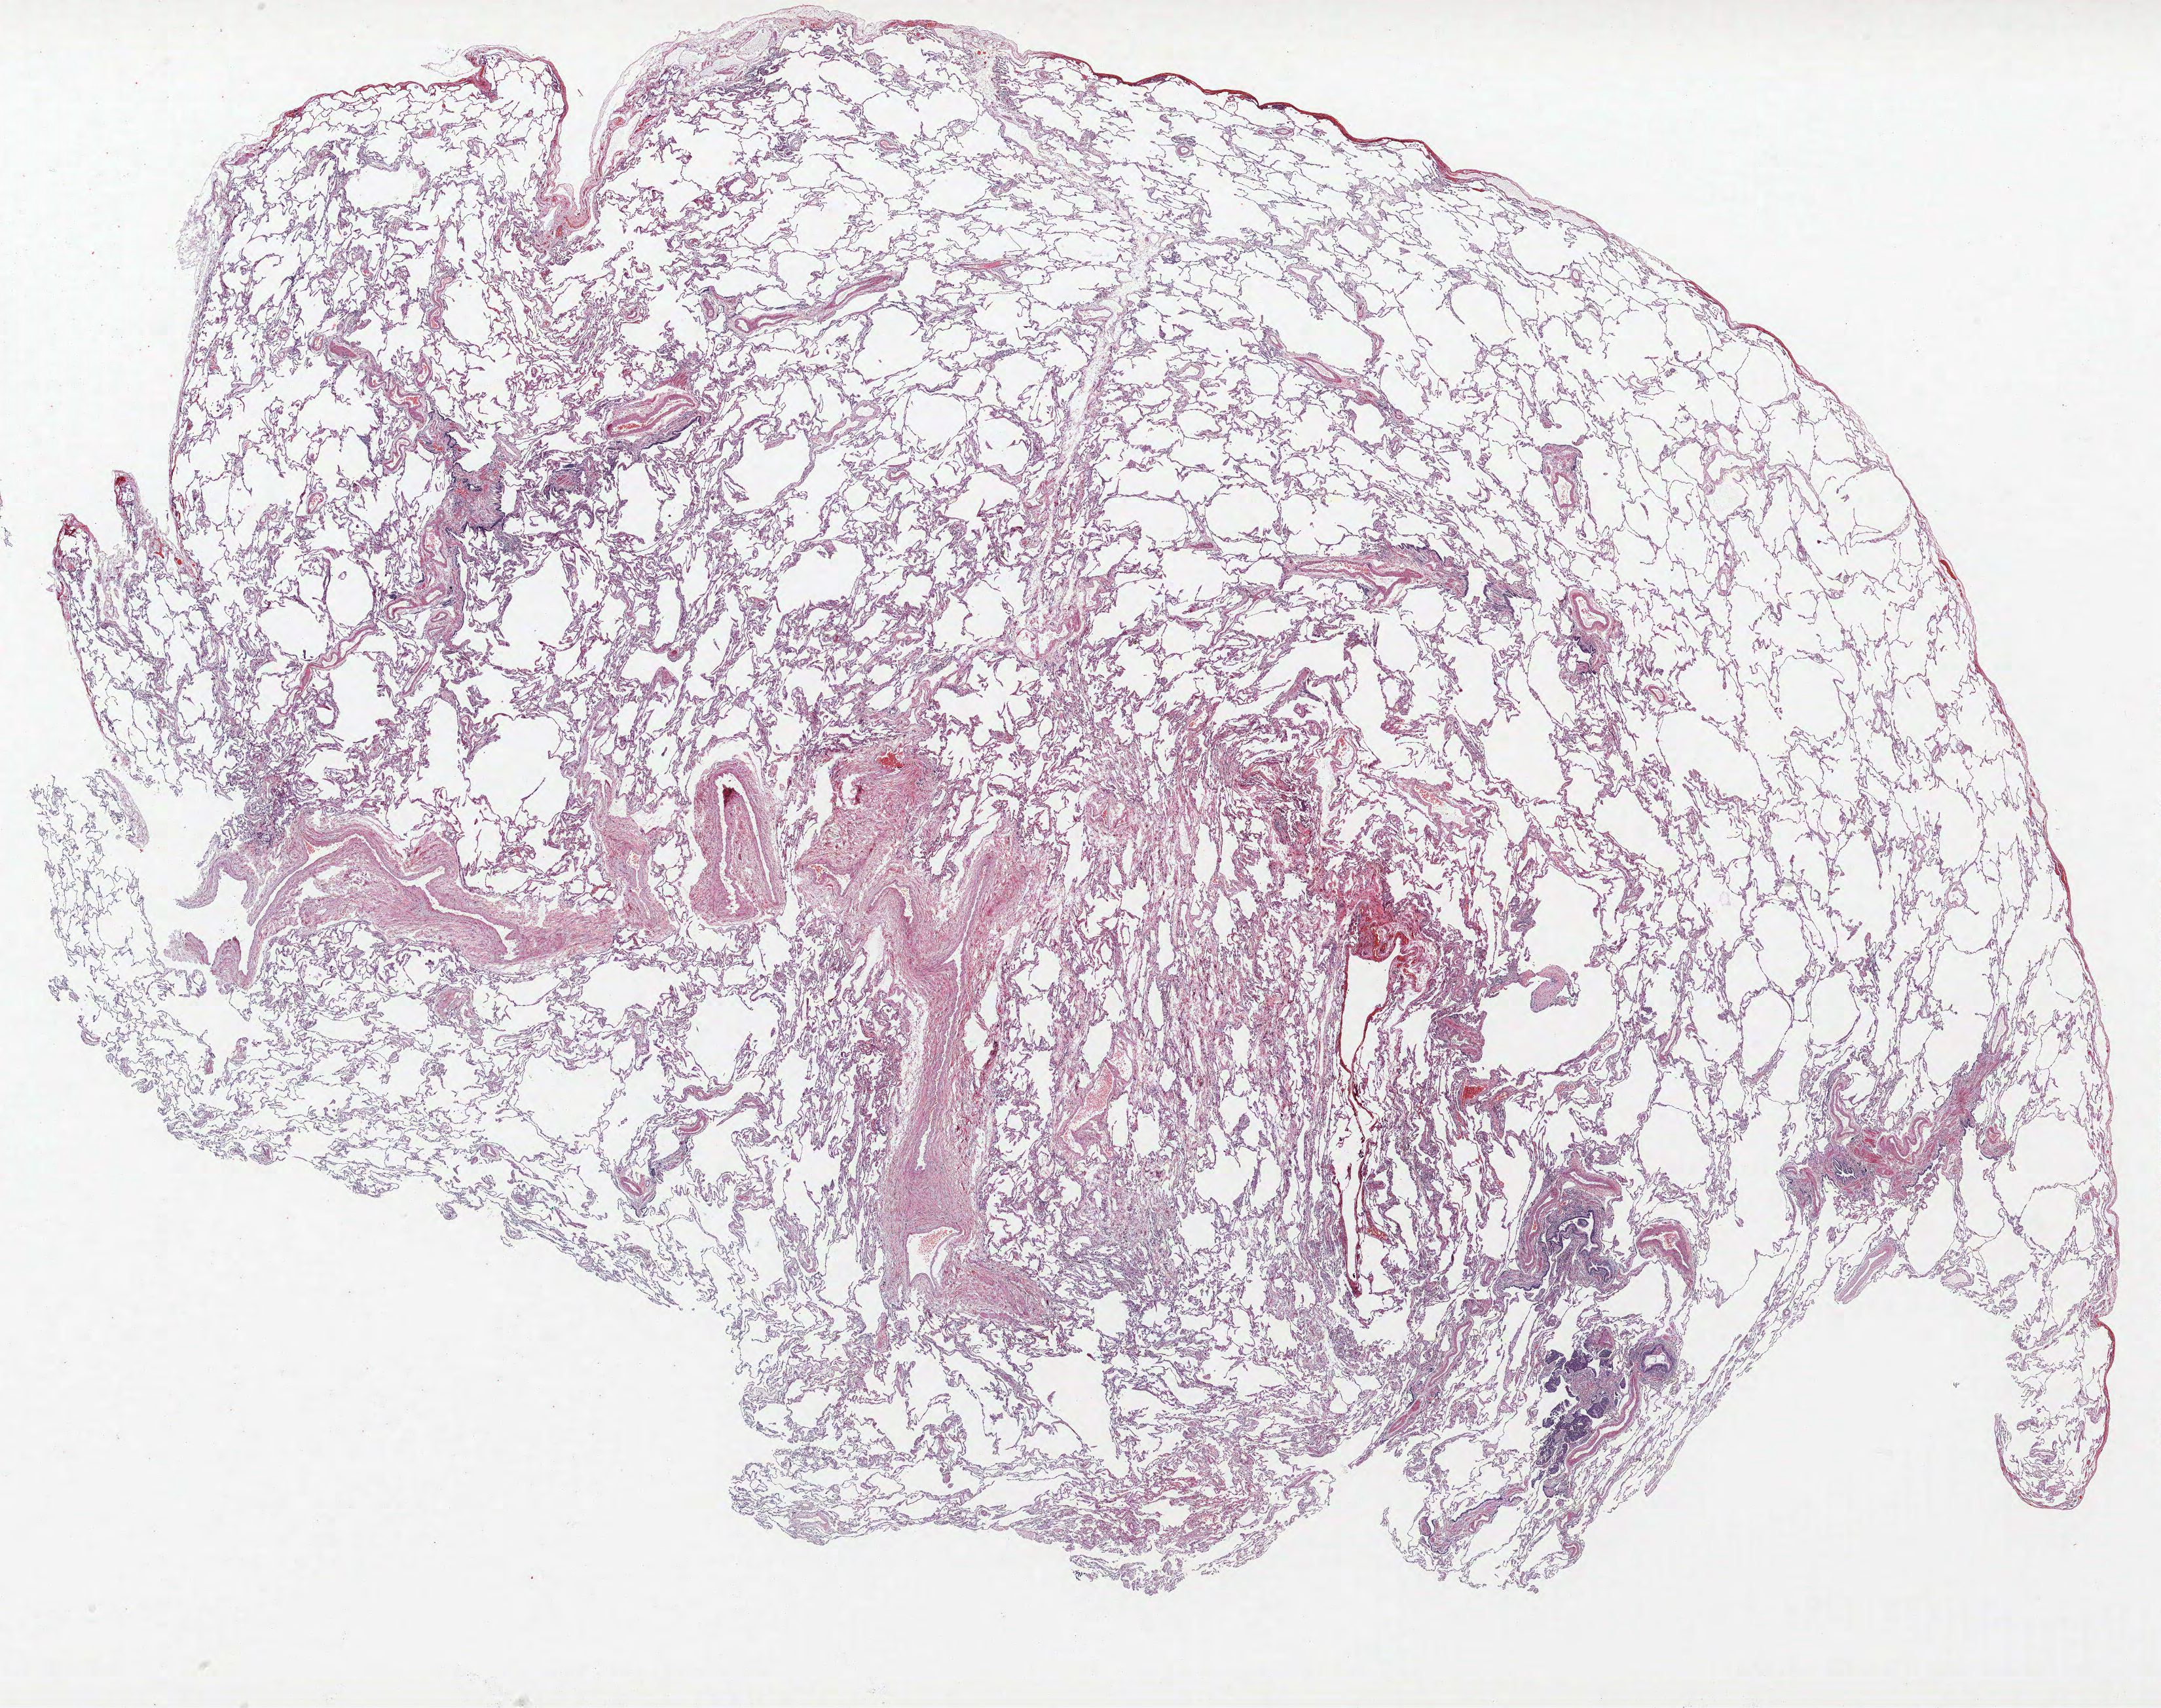
Whole-slide histology image, H&E — shown as a low-resolution overview of the whole scanned area (about 26.4 x 20.9 mm, from a 40x scan); formalin-fixed paraffin-embedded (FFPE) section; lung tissue. Male patient, aged 67 at enrolment. Grade: poorly differentiated (G3).
Participant's lung-cancer diagnosis: Adenocarcinoma, NOS. Tumour size (pathology): 80 mm. Primary tumour location (clinical record): left lower lobe. Stage (AJCC 6th edition): IB.